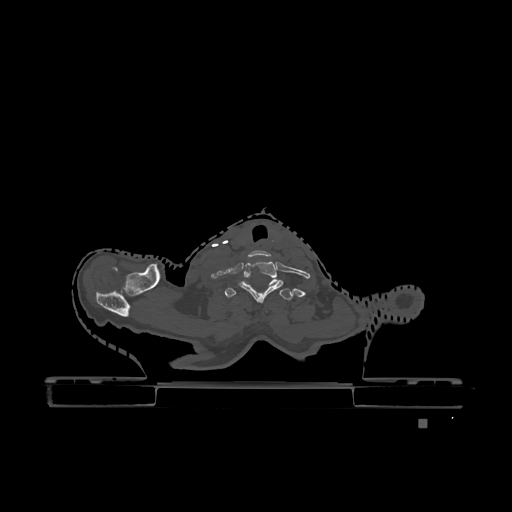
CT including the spine, one axial slice; slice 1021 of 1317 in the series (ordered by position); bone window (W 1800 / L 400 HU); 0.5 mm slice thickness; 512 × 512 image matrix, field of view 500 × 500 mm. Female patient, age 74 years. Case-level facts recorded for this patient, not image findings: primary cancer: lung; vertebrae with lytic lesions (as recorded): T1, T4, T5, T6, L4, L5.
Structures marked on this image (semi-automatically segmented with operator editing):
- T1 vertebra: bounding box (x1, y1, x2, y2) in pixels: (225, 281, 293, 300)